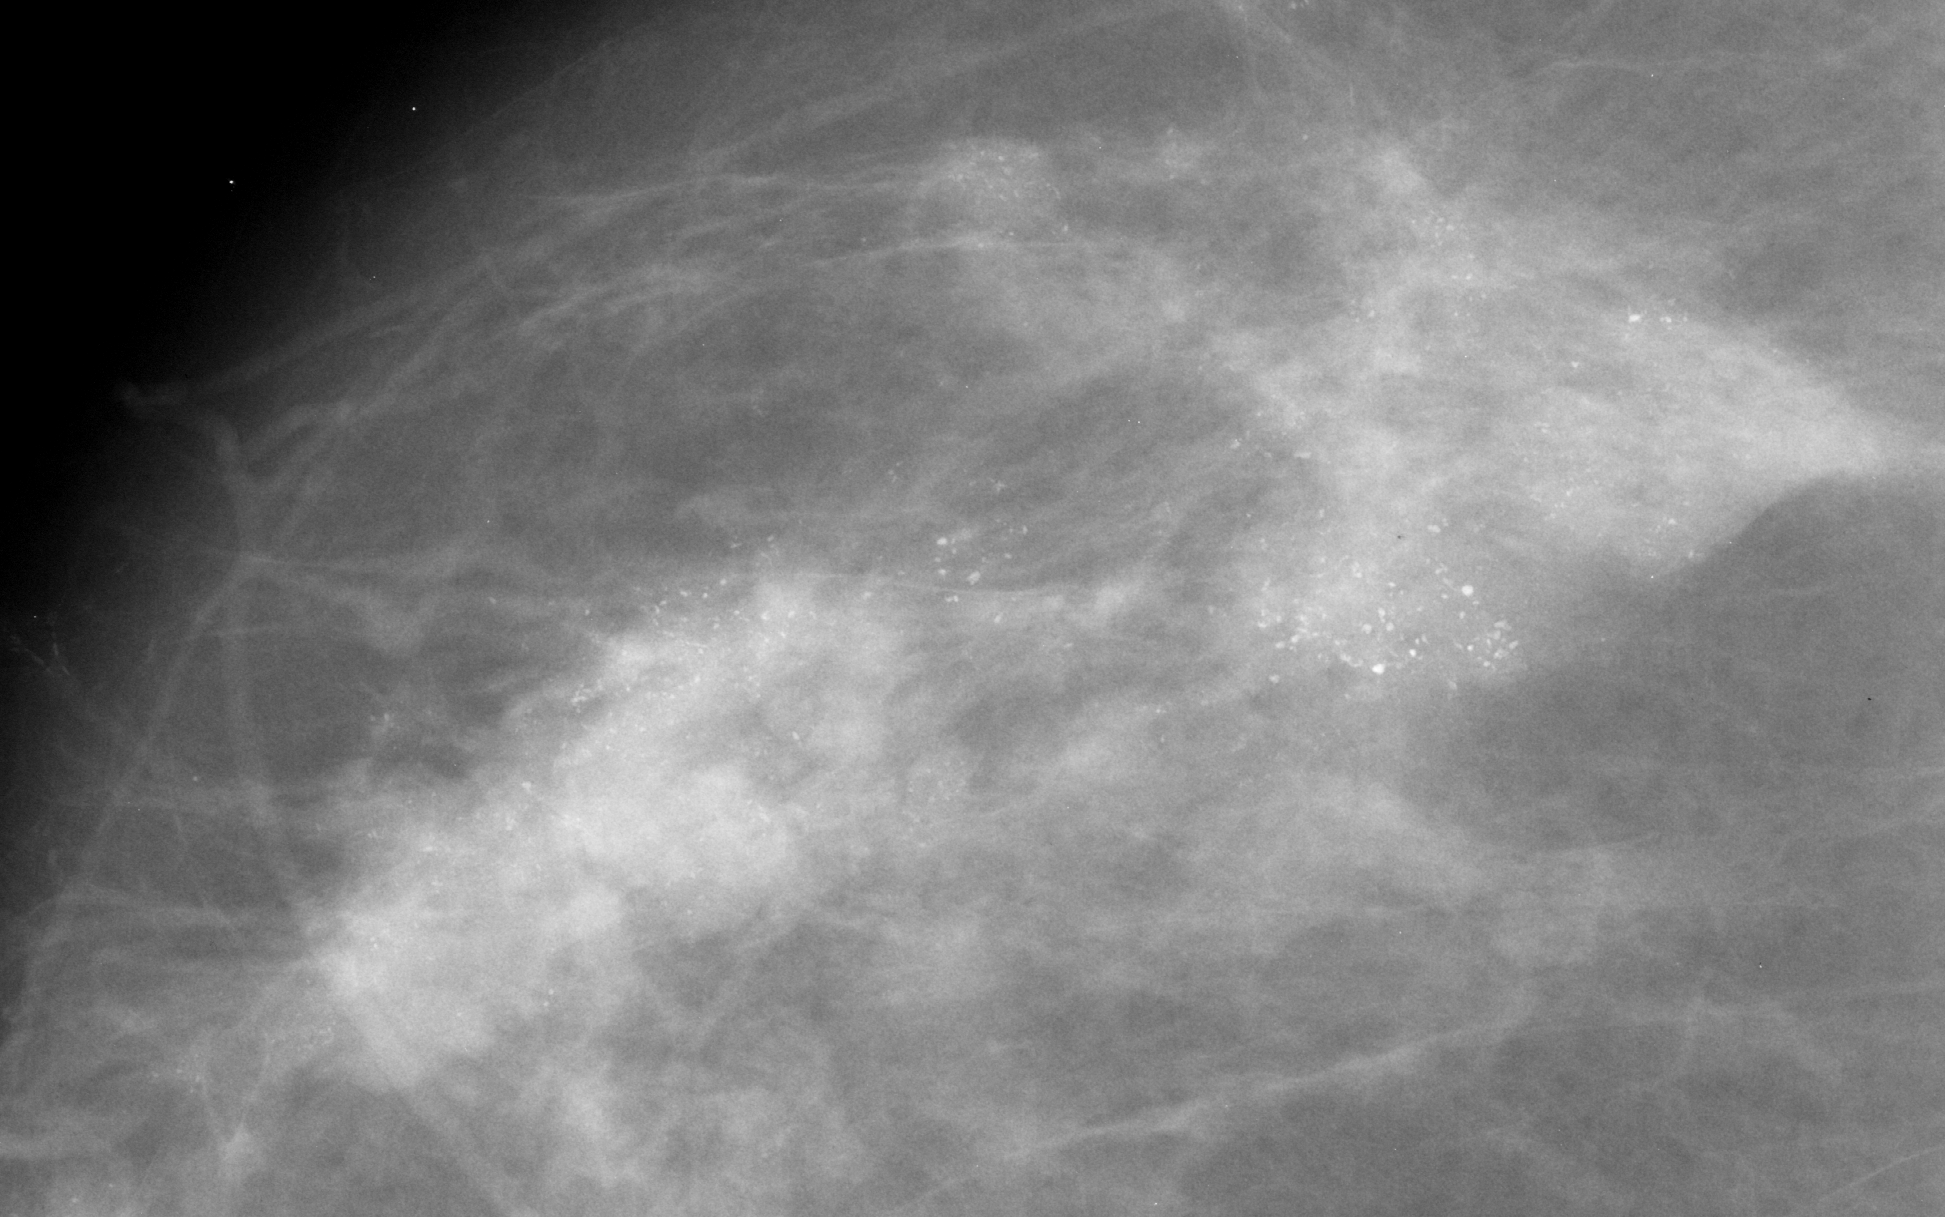
Cropped region of a digitized screen-film mammogram centred on a radiologist-marked abnormality; right breast; CC view; BI-RADS breast density category 2 (scale 1–4).
Calcifications, morphology pleomorphic, distribution regional; BI-RADS assessment category 5; pathology result (as recorded, not read from the image): malignant.